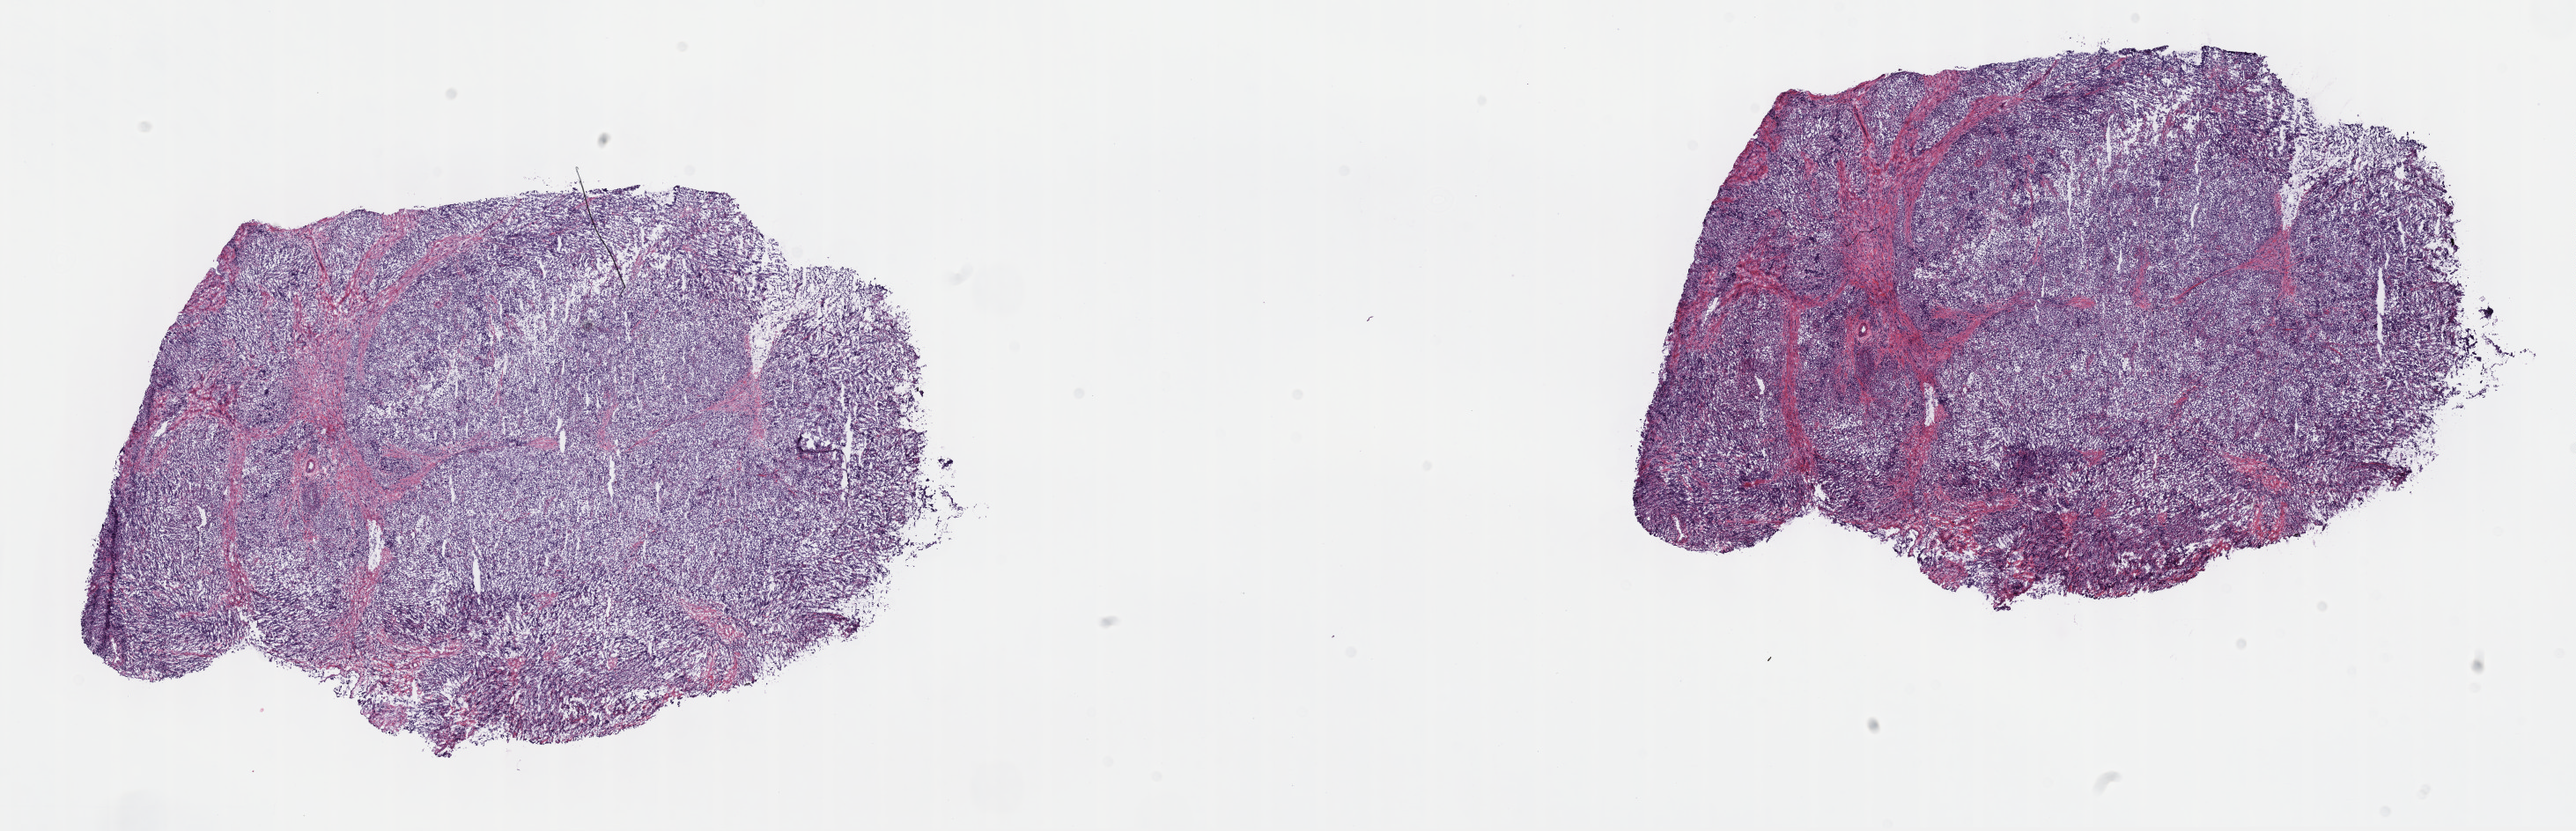
H&E whole-slide image, whole scanned area (about 23.7 x 7.6 mm, slide scanned at 40x) shown as a low-resolution overview. Frozen section from the top of the tissue portion. Sample: primary tumour, testis. Male patient; age at initial diagnosis 30 years. Composition of this section per pathologist review: tumour cells 100%, tumour nuclei 80%, normal cells 0%, stromal cells 0%, necrosis 0%. Inflammatory infiltration, as recorded: lymphocyte infiltration 2%, monocyte infiltration 0%, neutrophil infiltration 0%.
* AJCC pathologic stage: IS
* laterality: right
* TNM: T1 N0 M0
* diagnosis: Seminoma, NOS